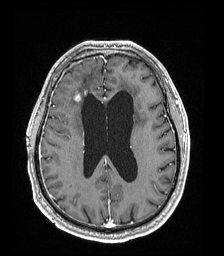
Brain MRI from a brain-tumour surgery series, one axial slice; position 75 of 192 along the scan axis; T1-weighted post-contrast; 1 mm slice thickness; 224 × 256 image matrix. Case-level facts recorded for this patient, not image findings: histopathology: Astrocytoma; WHO grade: 4; IDH mutation: yes; tumour location: Right Frontal.
Outlined on this slice (outlined manually by an expert reader):
- tumour: bounding box (x1, y1, x2, y2) in pixels: (75, 94, 81, 102)